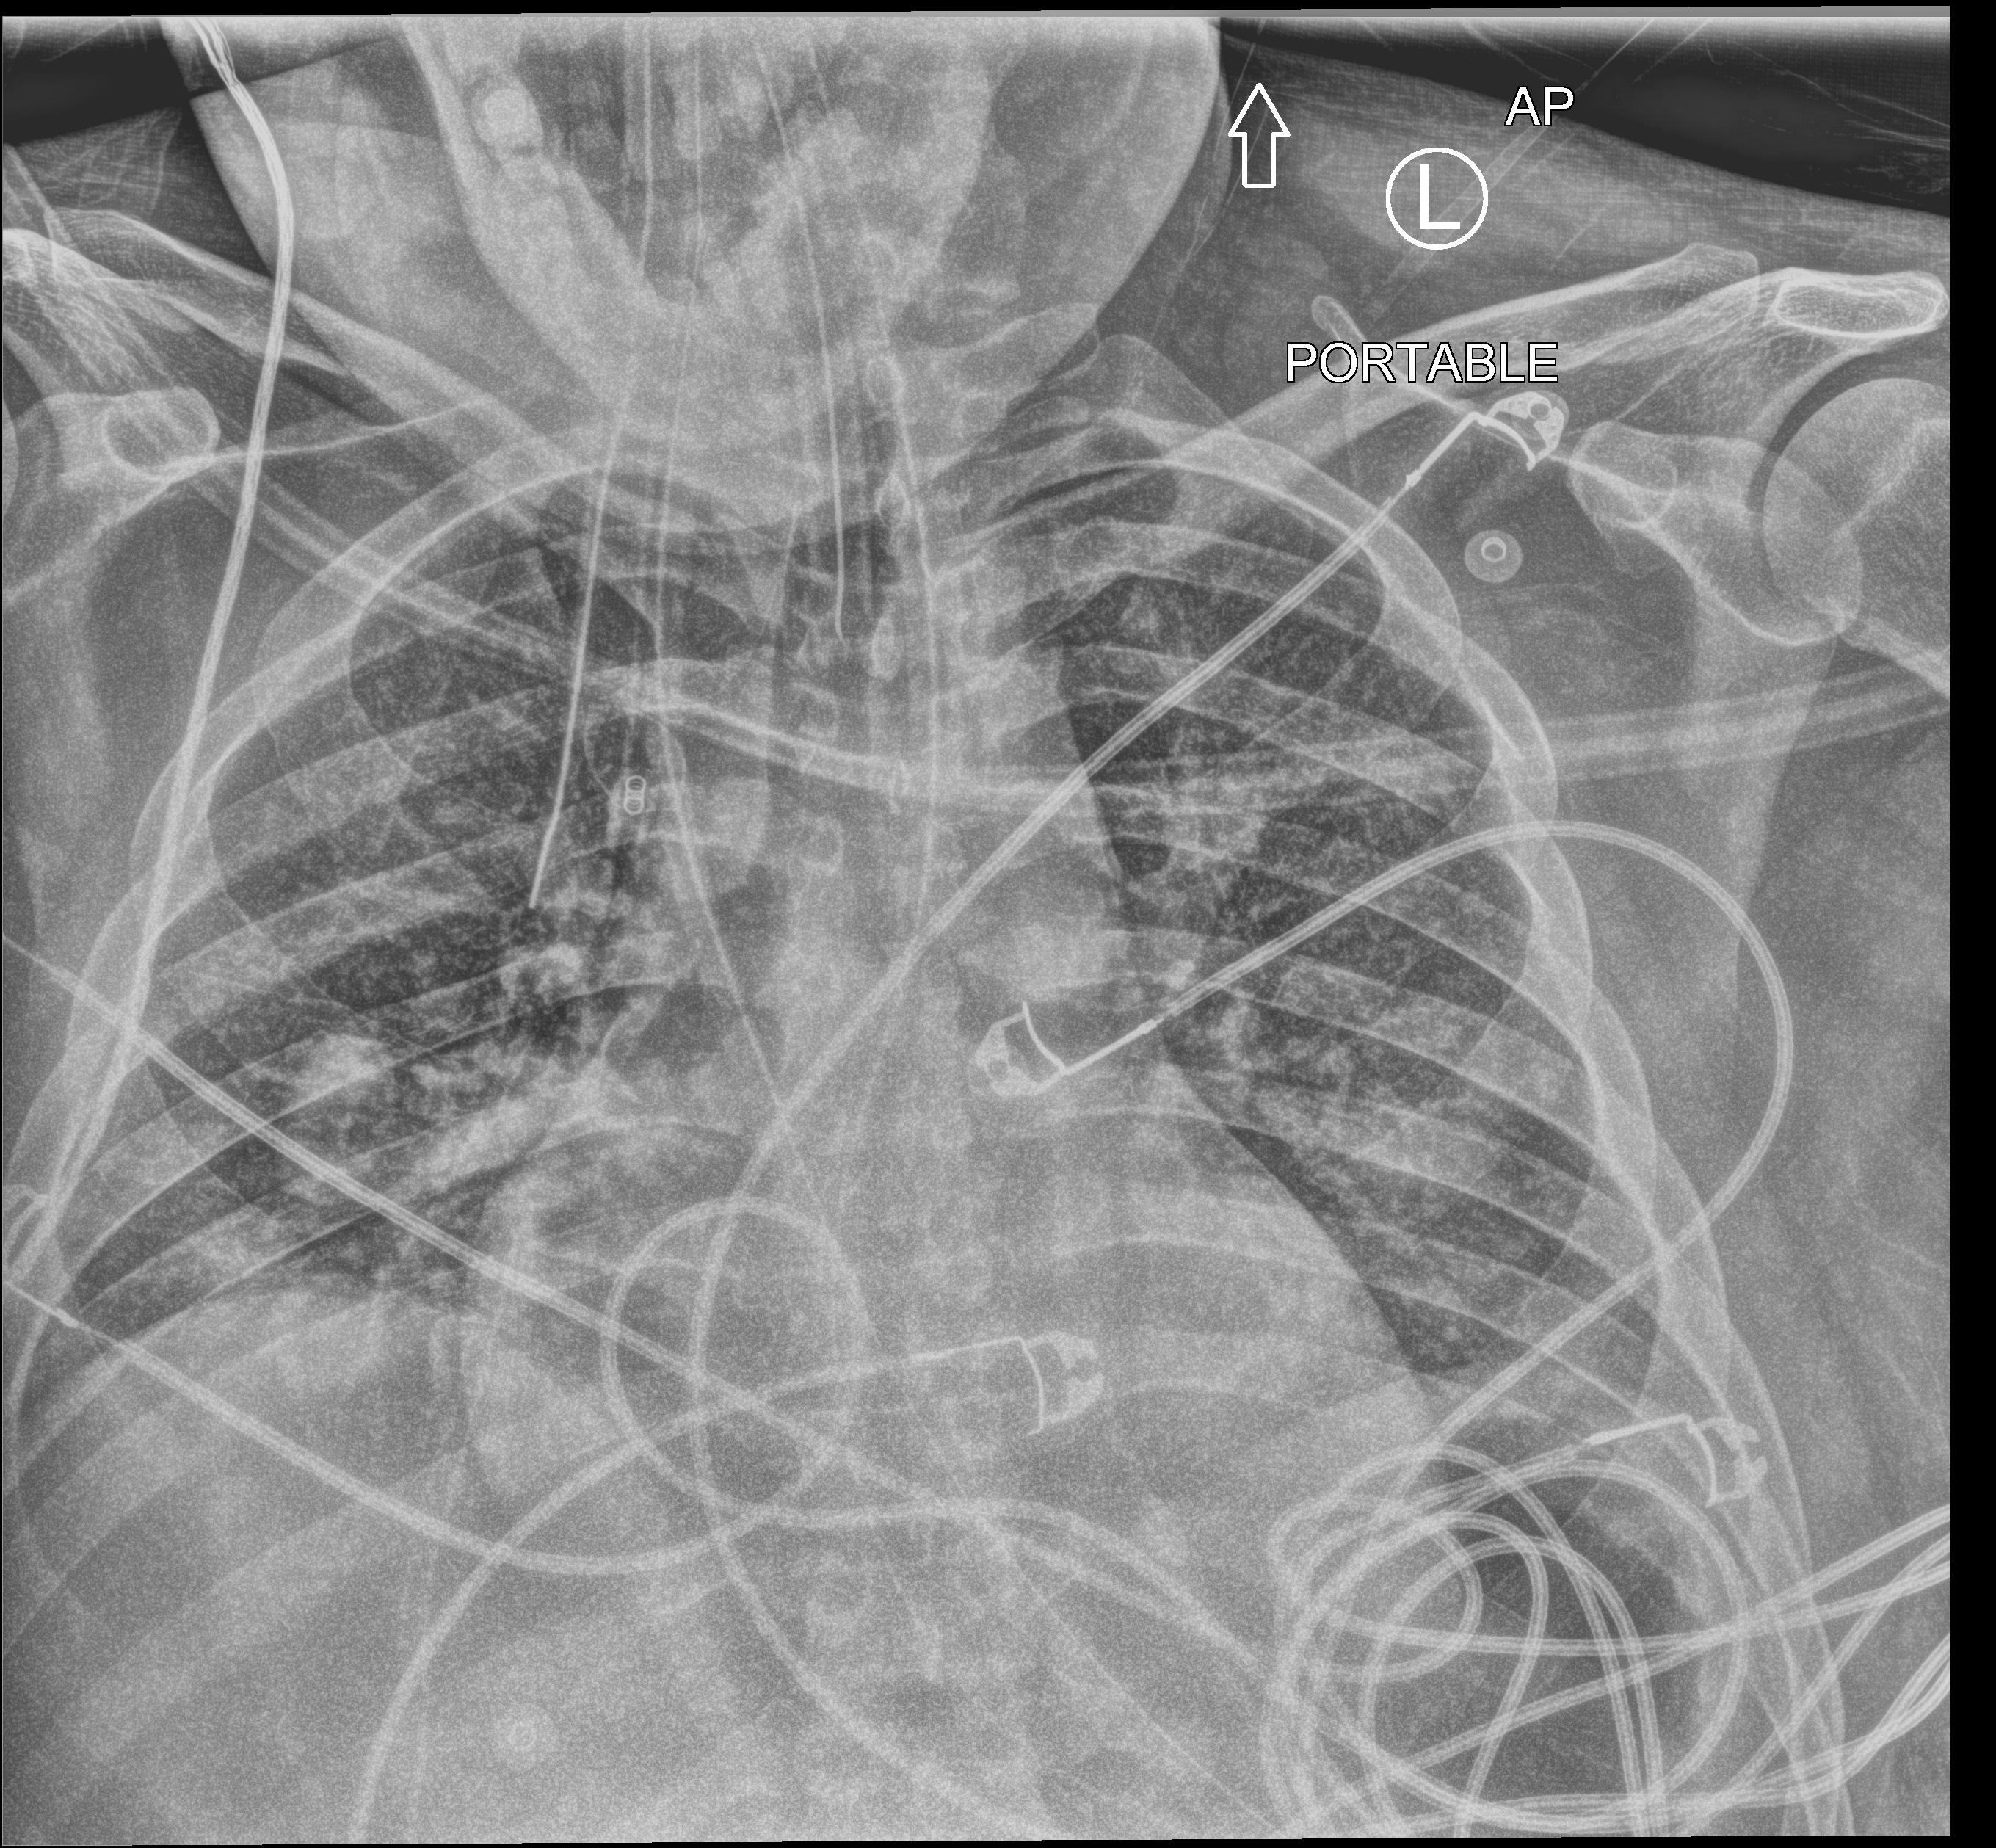
Chest X-ray (portable); anteroposterior (AP) projection. Male patient hospitalised with COVID-19, age 18–59 years.
From the hospital-stay record, not from the radiograph (when in the stay this image was taken is not recorded):
- other chronic lung disease (admission record): no